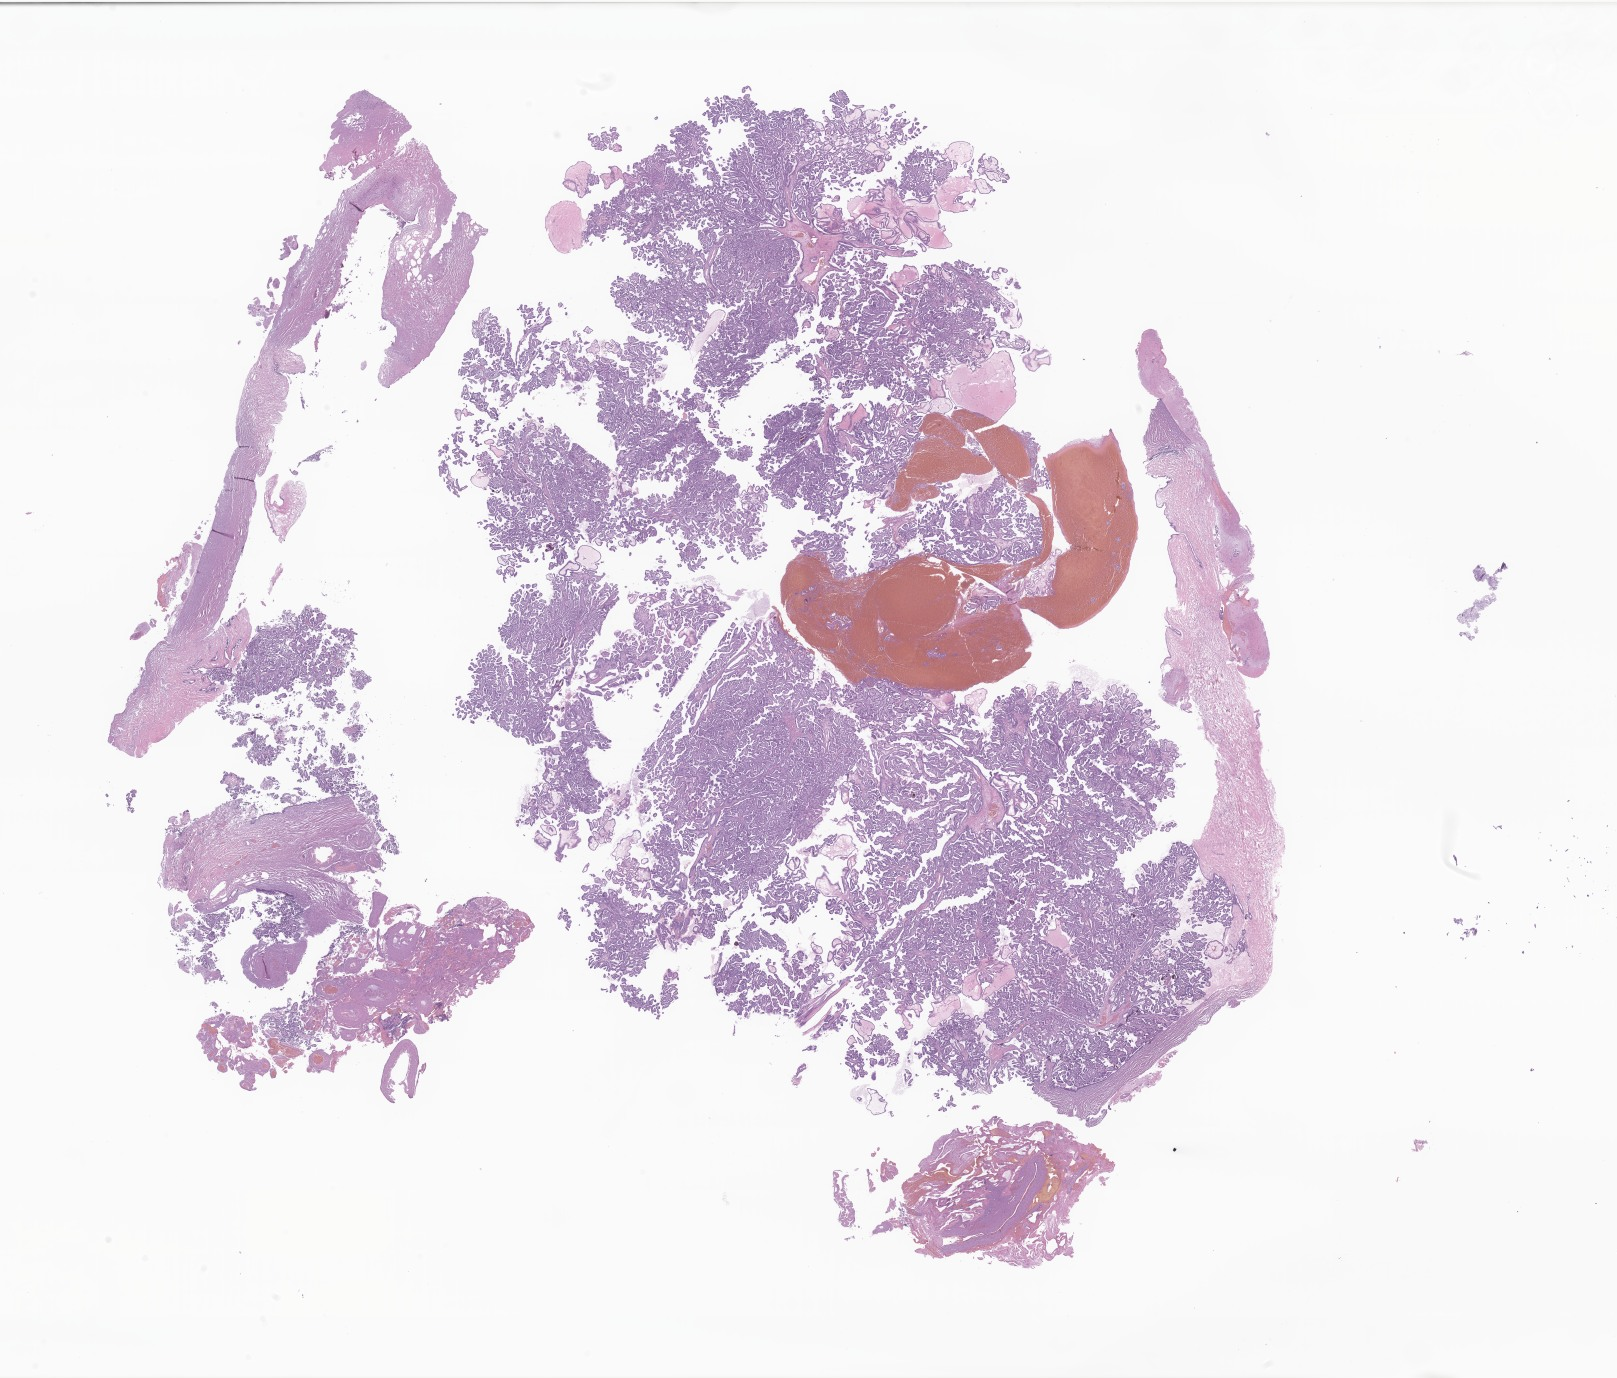
Digitized haematoxylin and eosin-stained section of tumor tissue from the brain, shown as a low-resolution overview of the whole scanned area (about 27.3 x 23.2 mm); formalin-fixed paraffin-embedded section. Patient male; age 43 months.
- diagnosis (ICD-O-3 morphology term): Choroid plexus papilloma, NOS